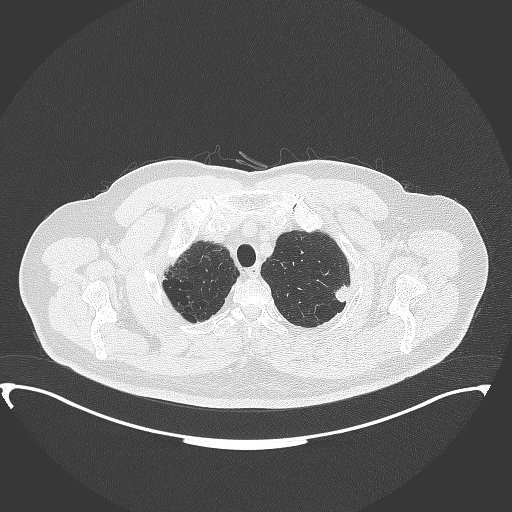
Chest CT, one axial slice. Position 325 of 350 along the scan axis. Reconstruction kernel B70f. Lung window (W 1500 / L -600 HU). 512 × 512 image matrix, field of view 459 × 459 mm. Patient: male, 64 years. From the clinical record (not read from this slice): clinical TNM (as recorded): T1c N1 M1.
Annotated regions visible in this slice (rectangle marked by the reading radiologist):
- lung tumour (recorded histology: adenocarcinoma): box from (x=332, y=277) to (x=356, y=309) px